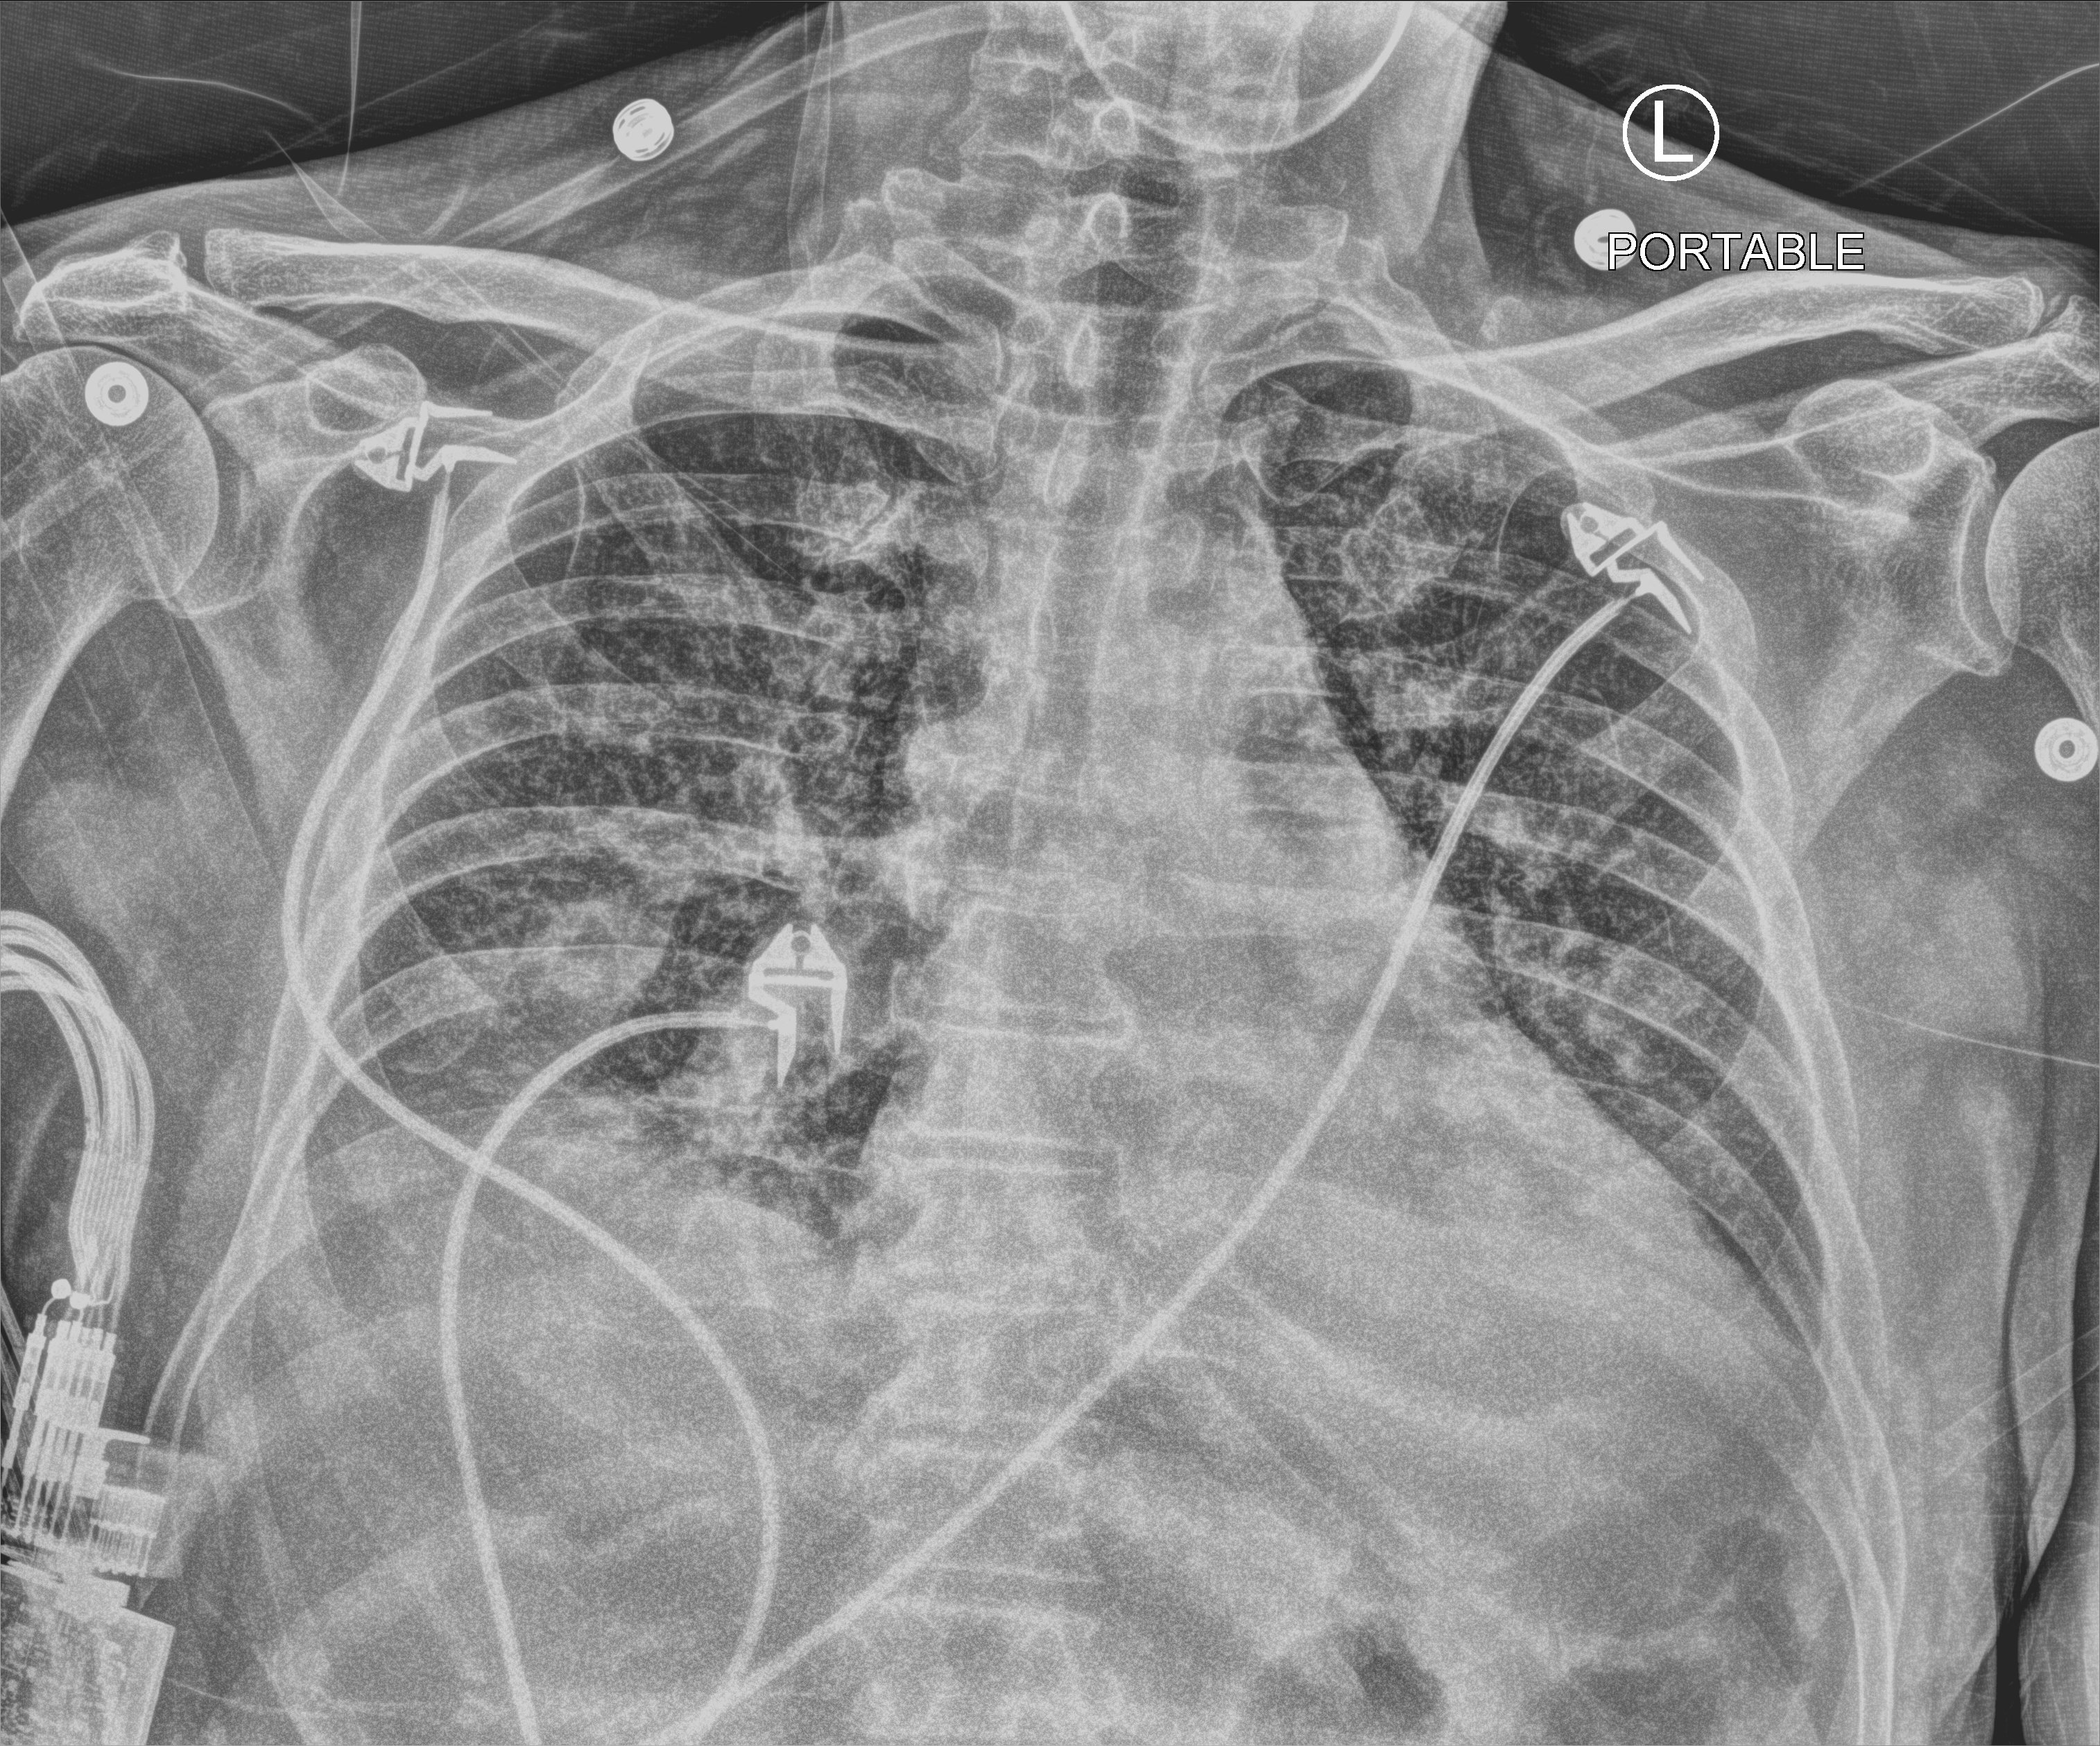
Bedside chest radiograph (computed radiography), anteroposterior (AP) projection. Male patient hospitalised with COVID-19, age 18–59 years.
Admission-level facts for this patient (not findings on this image; timing relative to this image not recorded):
- mechanically ventilated during this hospital stay: no